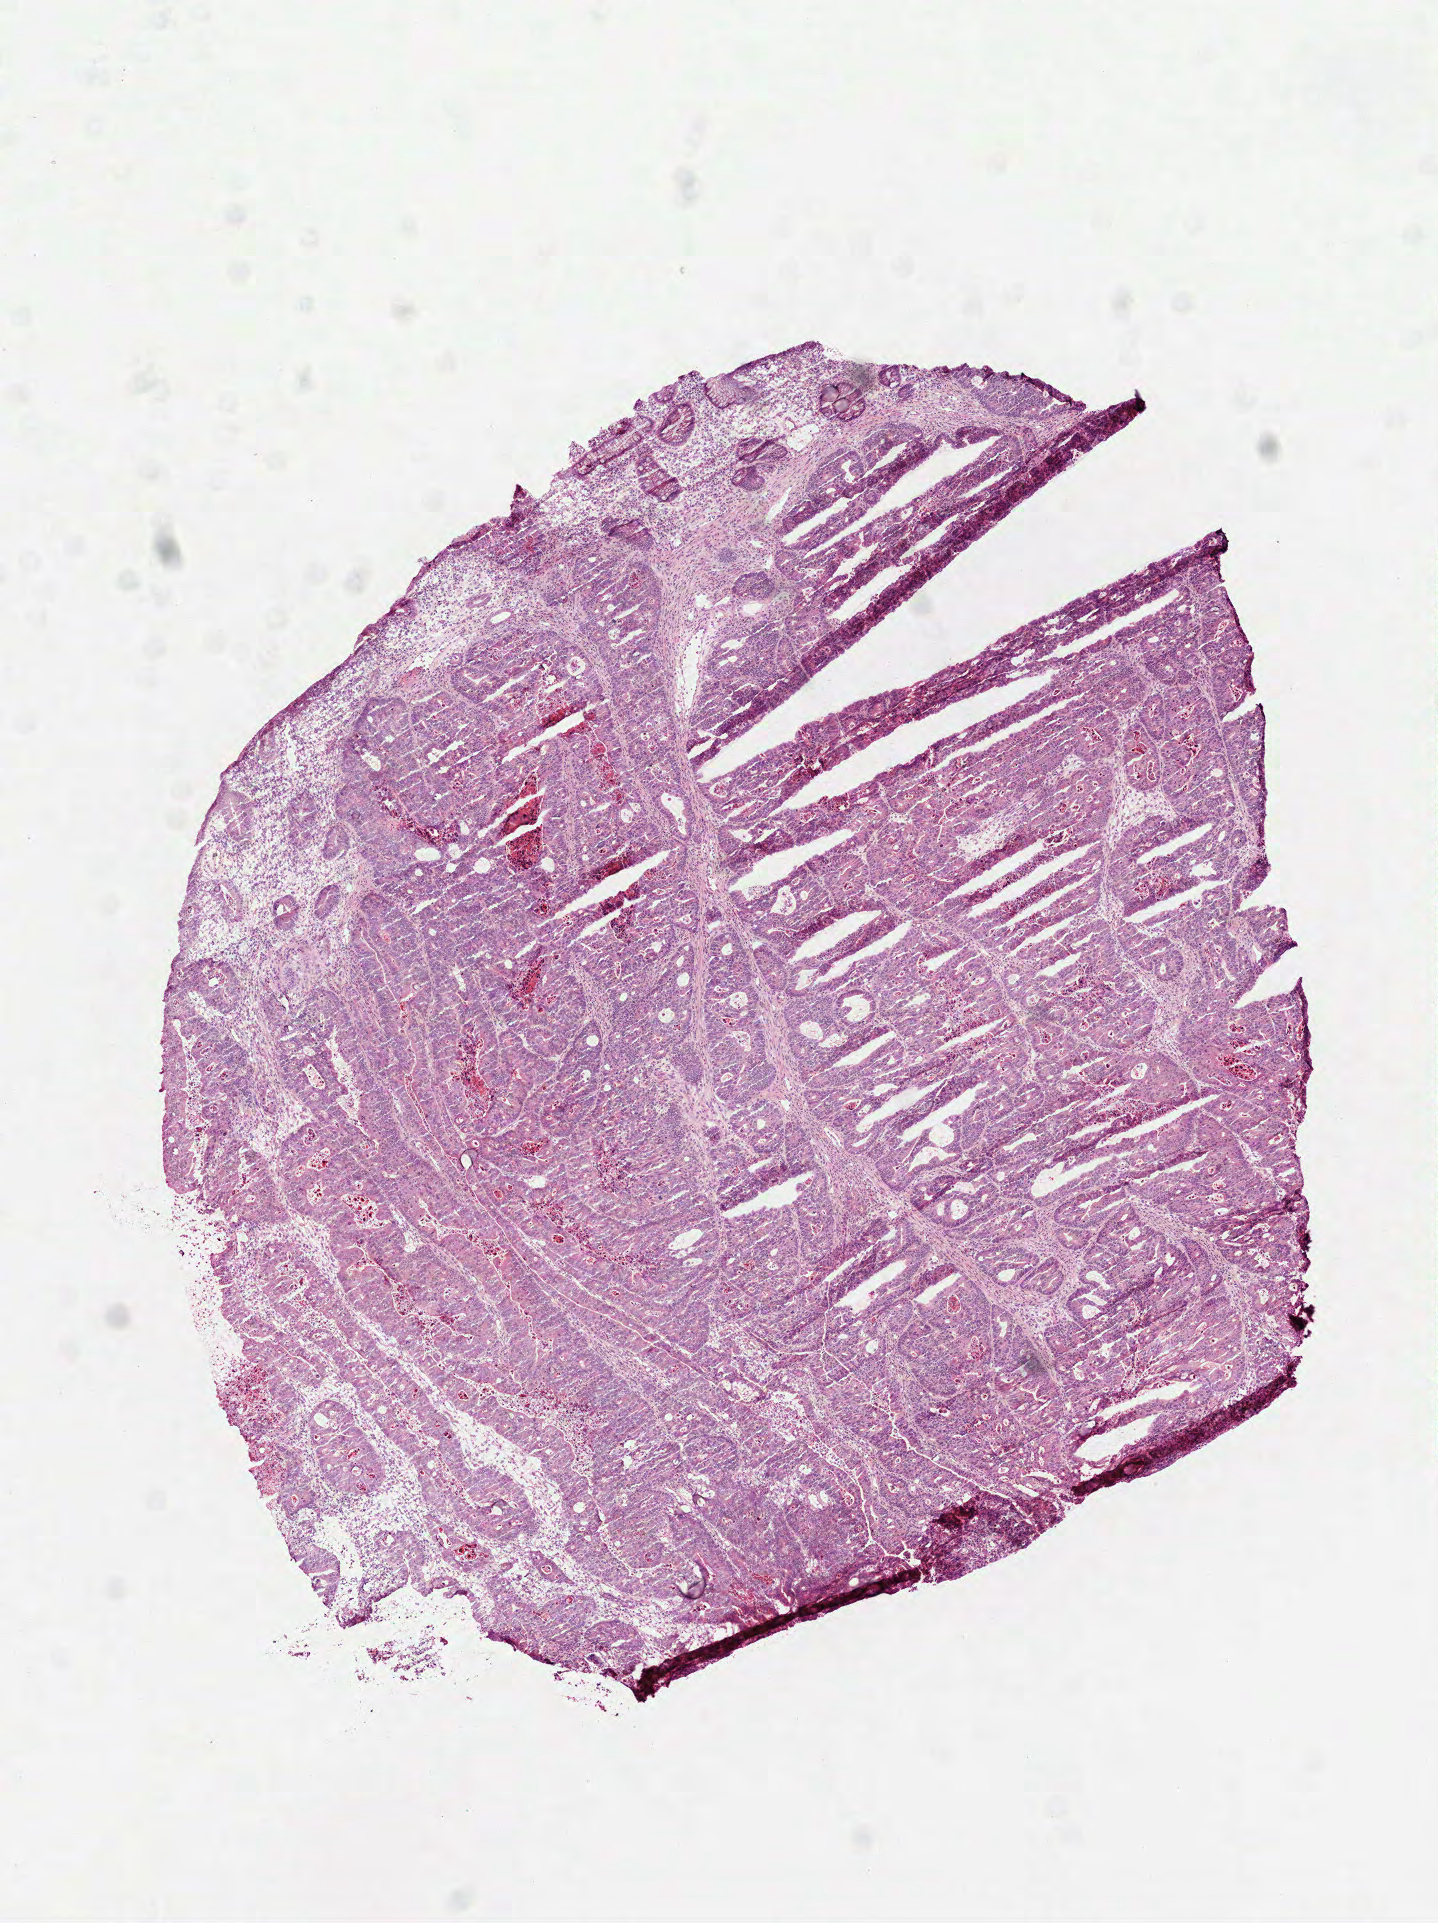
Digitized Hematoxylin and eosin (H&E) stained tissue section (whole slide) — shown as a low-resolution overview of the whole scanned area (about 5.8 x 7.8 mm, slide scanned at 40x); frozen section from the top of the tissue portion; sample: primary tumour, rectum. Female, age 64 years at initial diagnosis.
Pathologic diagnosis: Adenocarcinoma in tubulovillous adenoma.